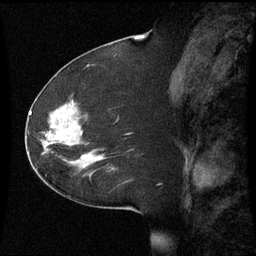
Breast MRI (dynamic contrast-enhanced), one sagittal slice; slice 29 of 60 in the series (ordered by position); dynamic contrast-enhanced series, image 2 of 3 at this slice position (ordered by acquisition); 1.5 T; TE 4.2 ms, TR 8.9 ms; 2.2 mm slice thickness; 256 × 256 image matrix, field of view 220 × 220 mm. Patient: female, 51 years. From the clinical record (not read from this slice): setting: breast cancer imaged before/during neoadjuvant chemotherapy; receptor status: HR-positive, HER2-negative.
Structures marked on this image (semi-automatic segmentation, software-assisted and operator-edited):
- analysis volume of interest (the breast-tissue region the enhancement analysis was run in; not a lesion): bounding box <44,102,107,169> (left, top, right, bottom; pixels)
- tumour enhancement mask (voxels above the 70 % enhancement threshold inside the analysis volume of interest): <52,126,101,159>